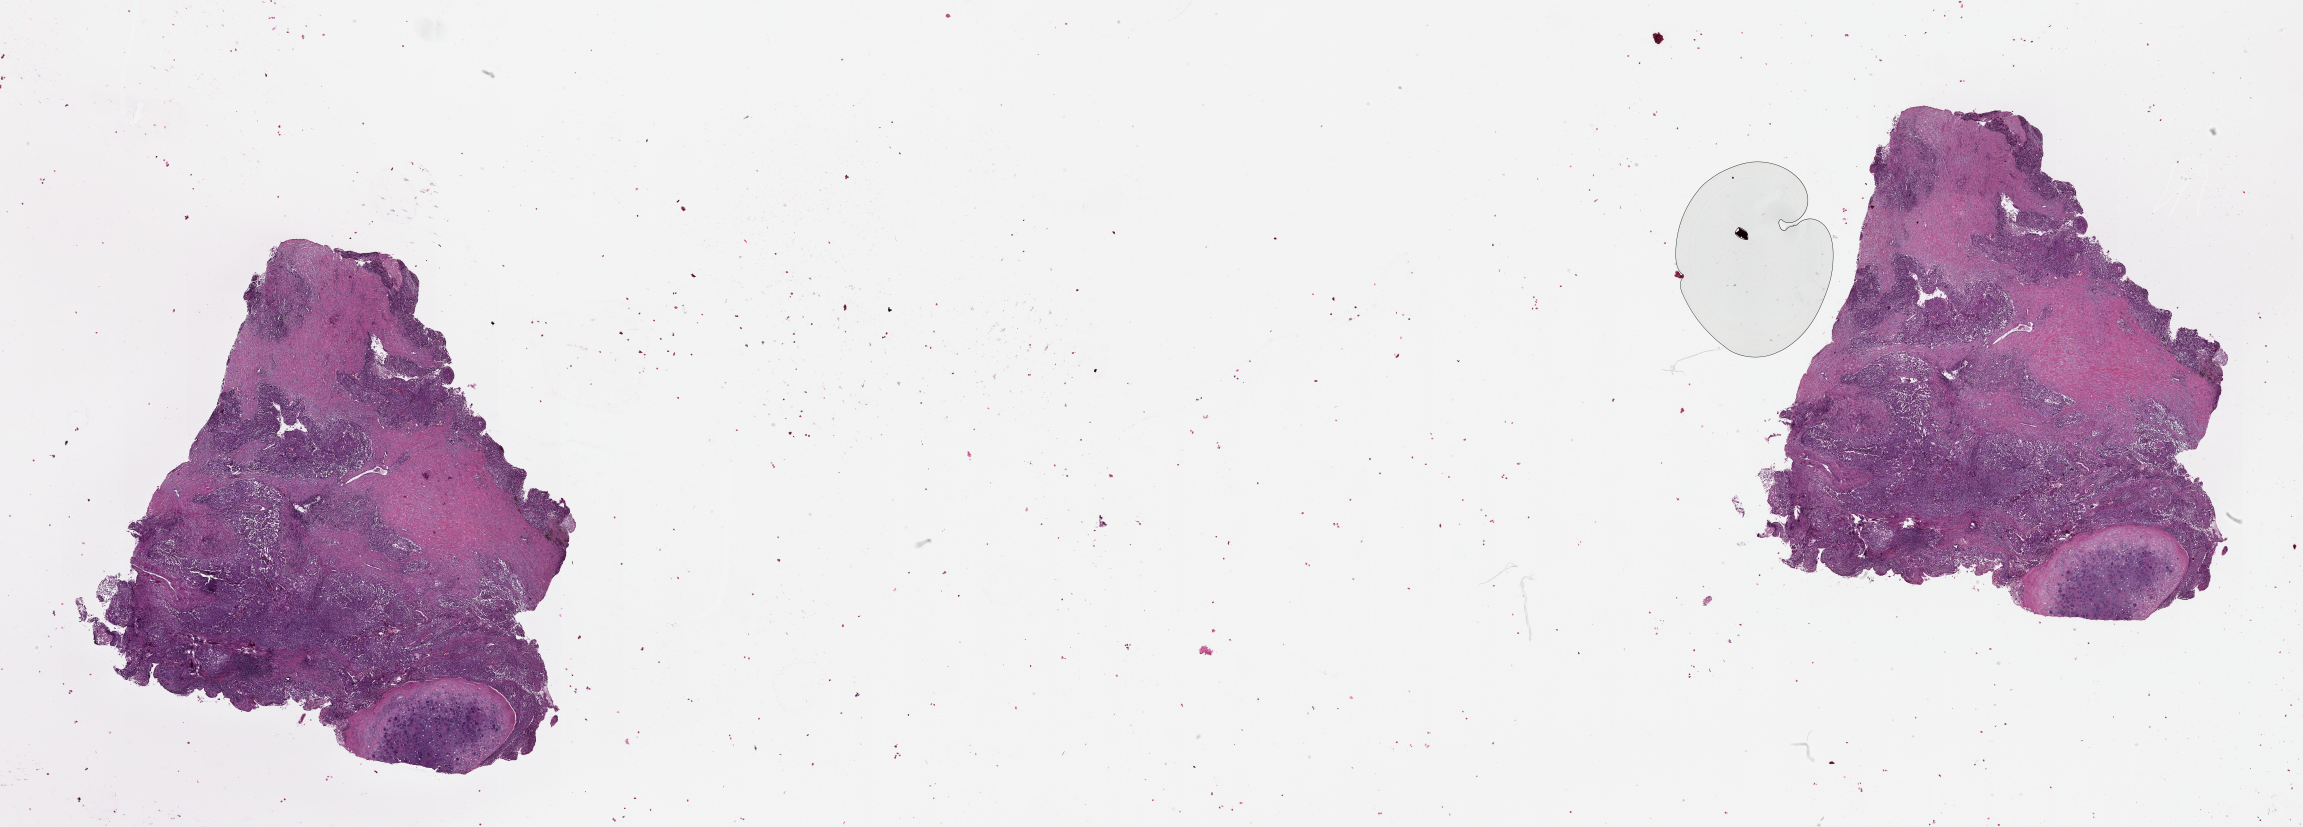
Hematoxylin and eosin (H&E) stained whole-slide image — shown as a low-resolution overview of the whole scanned area (about 37.1 x 13.3 mm, slide scanned at 20x), tumour tissue sample, lung. 65-year-old male patient.
Patient diagnosis (cohort enrolment): squamous cell carcinoma (lung).